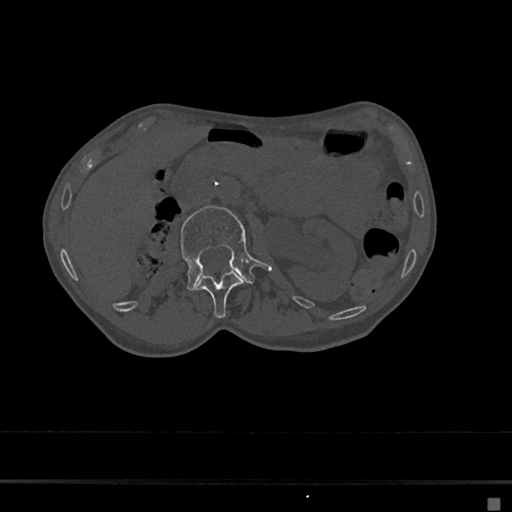
CT including the spine, one axial slice; slice 36 of 797 in the series (ordered by position); reconstruction kernel Br40s/3; 120 kVp; bone window (W 1800 / L 400 HU); 0.5 mm slice thickness; 512 × 512 image matrix, field of view 360 × 360 mm. Patient: female, 68 years. From the clinical record (not read from this slice): primary cancer: renal.
Outlined on this slice (semi-automatically segmented with operator editing):
- L1 vertebra: bounding box [x1, y1, x2, y2] px = [196, 270, 244, 319]
- L2 vertebra: [180, 205, 271, 290]